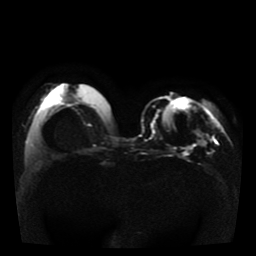
Breast MRI, one axial slice. Position 14 of 41 along the scan axis. Diffusion-weighted series; image 2 of 4 stored at this slice position (different b-values; order by instance number). 1.5 T. 5 mm slice thickness. 256 × 256 image matrix, field of view 330 × 330 mm. Female patient.
Structures marked on this image (expert manual segmentation):
- tumour on diffusion-weighted imaging: bounding box (x1, y1, x2, y2) in pixels: (187, 131, 204, 149)